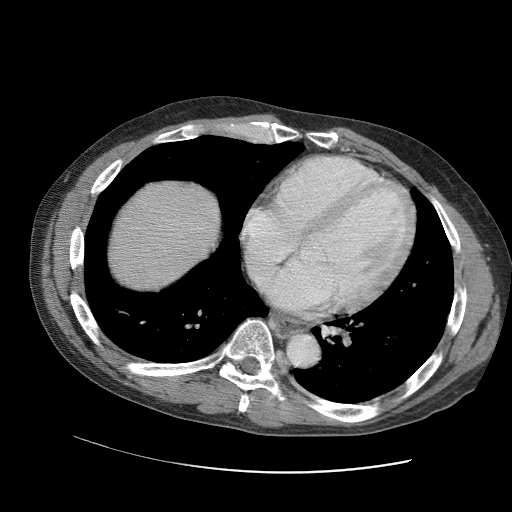
Contrast-enhanced abdominal CT (liver protocol), one axial slice; slice 96 of 109 in the series (ordered by position); soft-tissue window (W 400 / L 40 HU); 2.5 mm slice thickness; 512 × 512 image matrix, field of view 400 × 400 mm. From the clinical record (not read from this slice): diagnosis: hepatocellular carcinoma (patient treated with transarterial chemoembolisation; whether this scan precedes or follows treatment is not stated here); TNM stage (as recorded): Stage-IIIC; Child-Pugh class: B; tumour nodularity: uninodular.
Structures marked on this image (semi-automatic segmentation, software-assisted and operator-edited):
- liver parenchyma outside the tumour (the mass and vessels are separate outlines, so this box may not span the whole liver): box from (x=106, y=180) to (x=220, y=290) px